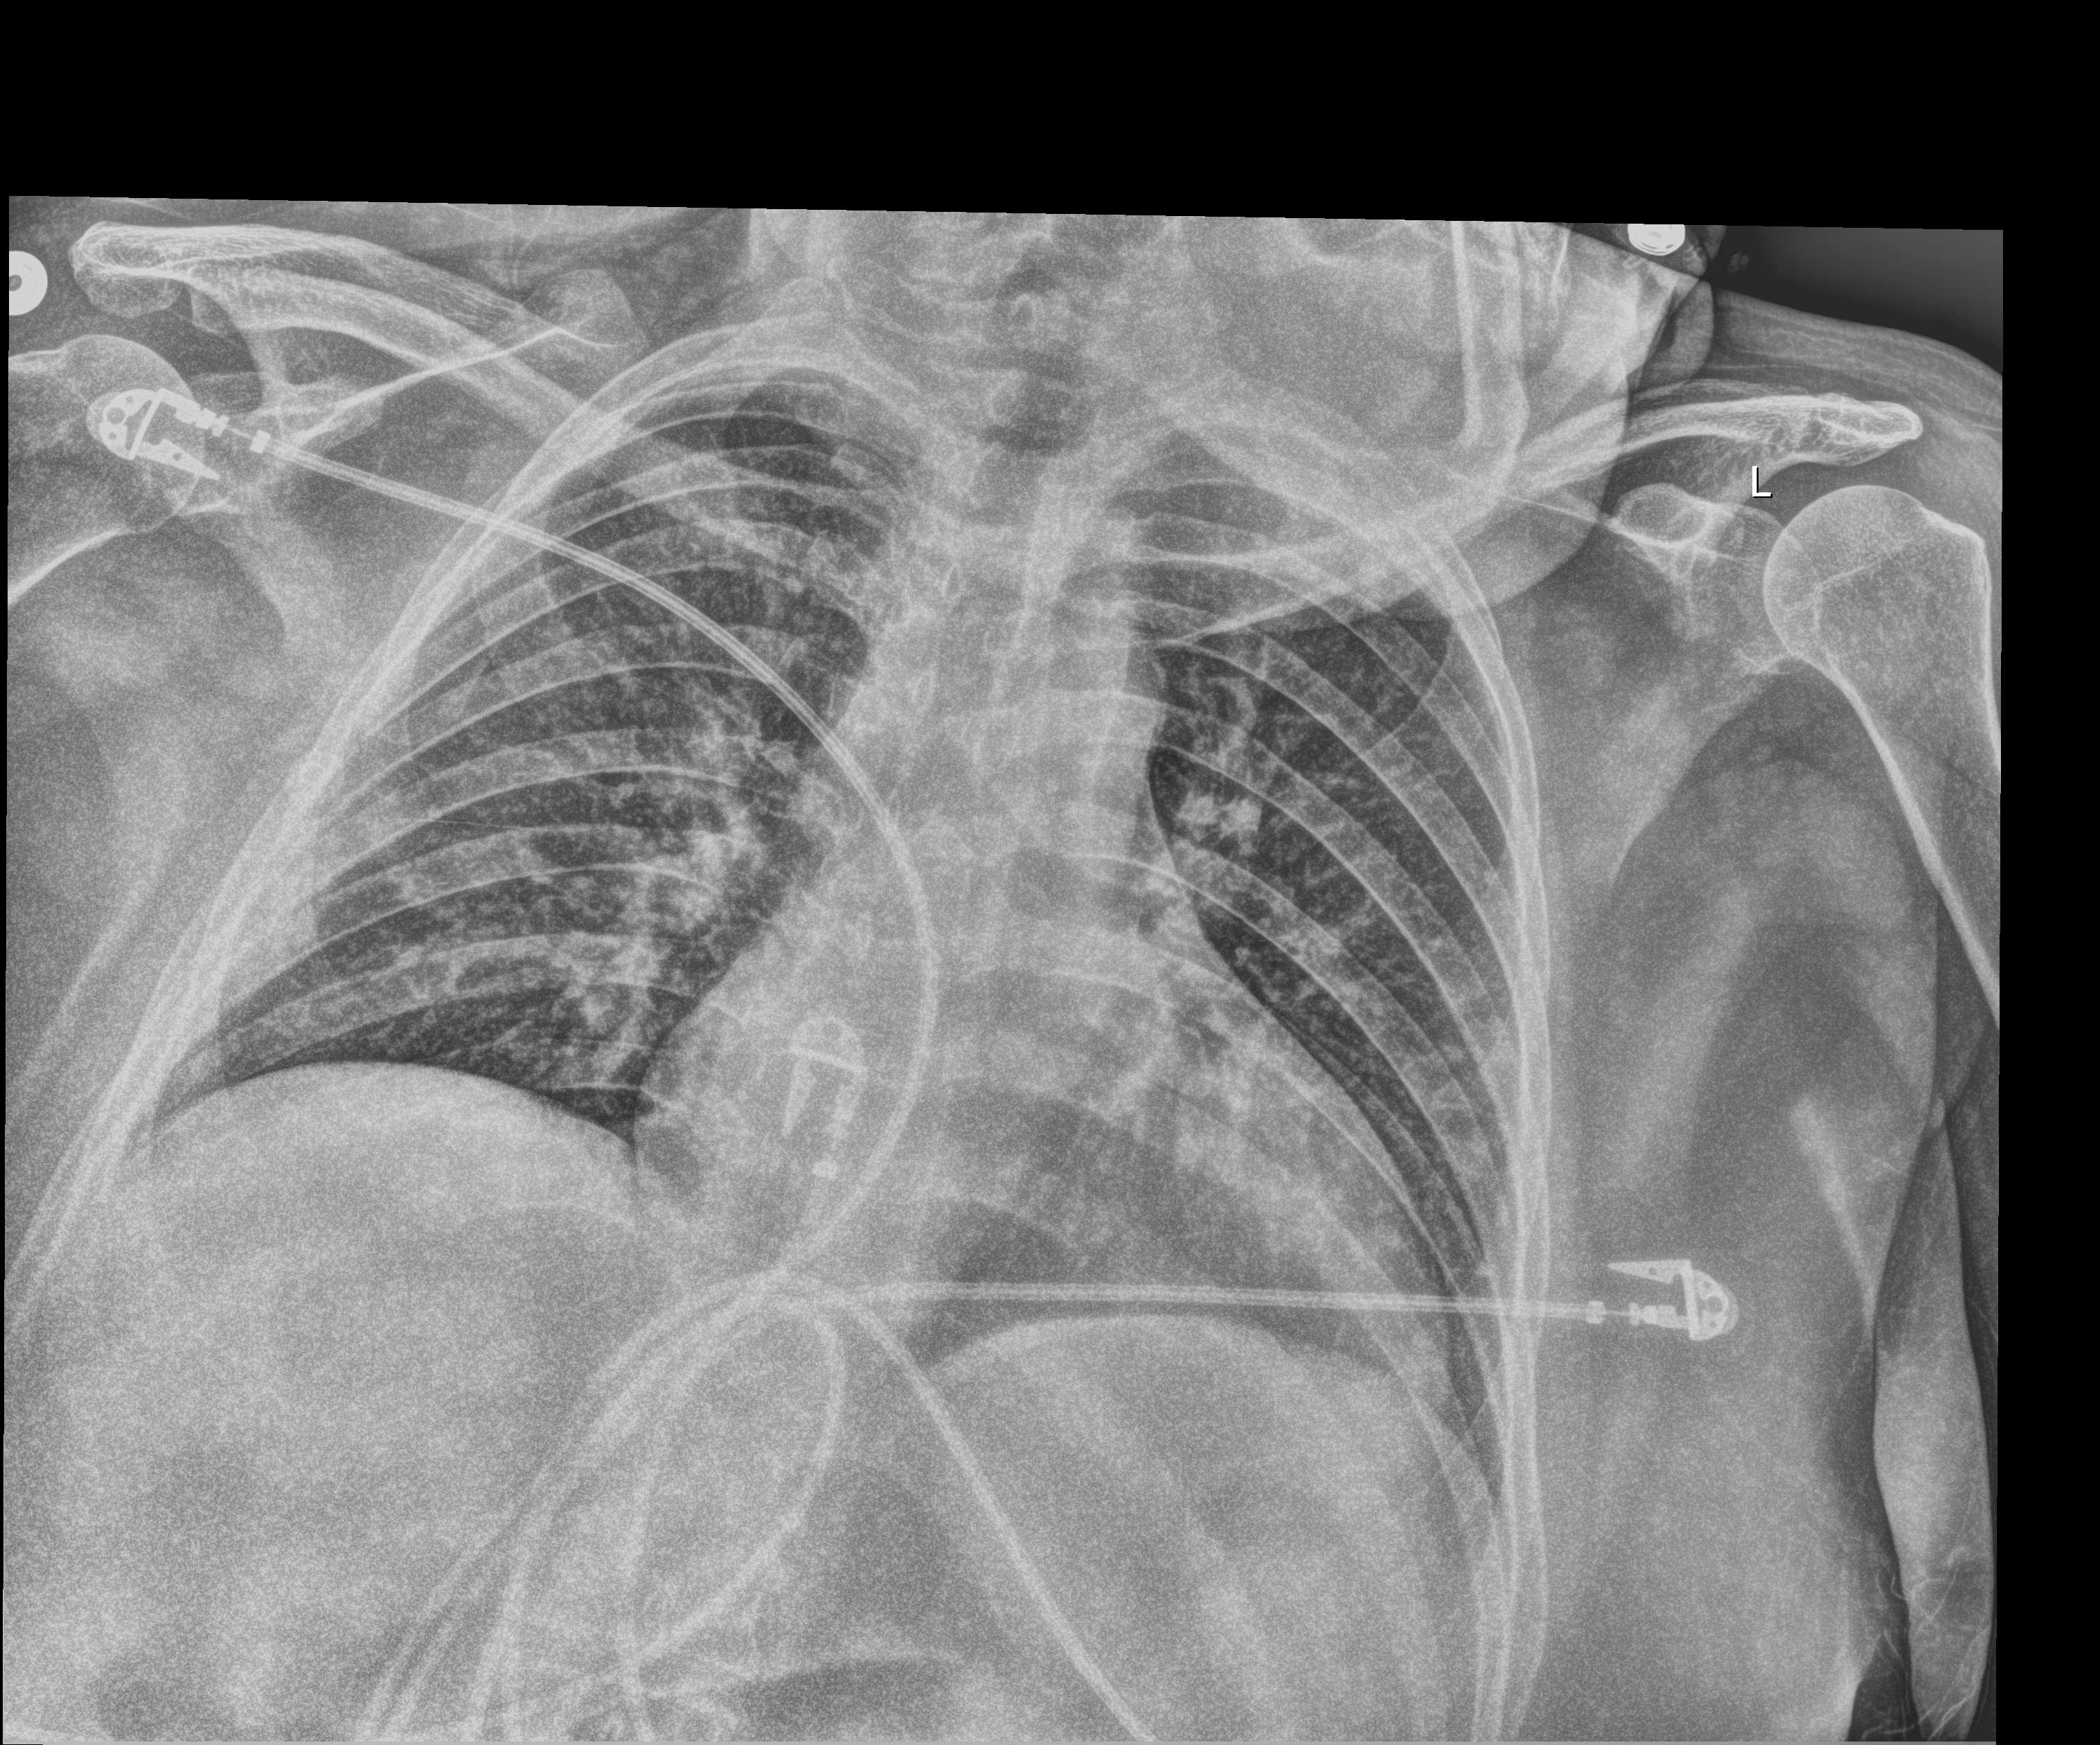
Portable chest radiograph. Female patient hospitalised with COVID-19, age 60–74 years.
From the hospital-stay record, not from the radiograph (when in the stay this image was taken is not recorded): admitted to intensive care during this hospital stay: no; length of hospital stay: 9 days; mechanically ventilated during this hospital stay: no.